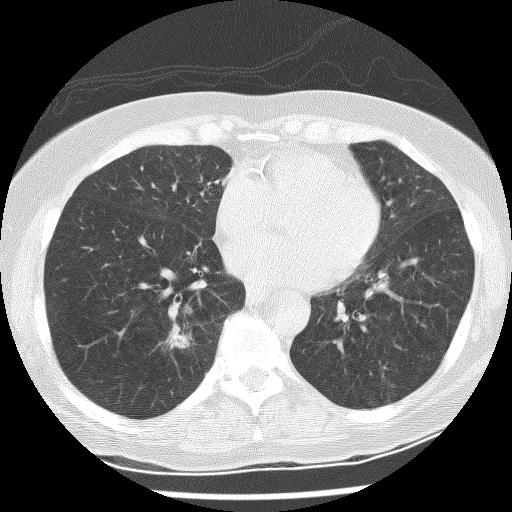
Chest CT (low-dose screening protocol), one axial image, baseline screening round, lung window (W 1500 / L -600 HU), lung (sharp) reconstruction kernel (BONE), 512 × 512 image matrix. Female participant, aged 60 years at enrolment. Former smoker at enrolment.
- Expert-annotated lung lesion, box from (x=156, y=322) to (x=203, y=358) px.
- Screening reader's record for this exam (one nodule recorded; not confirmed to be the boxed lesion): non-calcified nodule or mass ≥4 mm, right lower lobe, 10 × 6 mm, spiculated (stellate) margins, mixed attenuation.
- Later outcome: lung cancer diagnosed 275 days after this screen — adenocarcinoma with squamous metaplasia, right lower lobe, poorly differentiated (G3), stage IA (AJCC 6th edition), 23 mm at pathology.